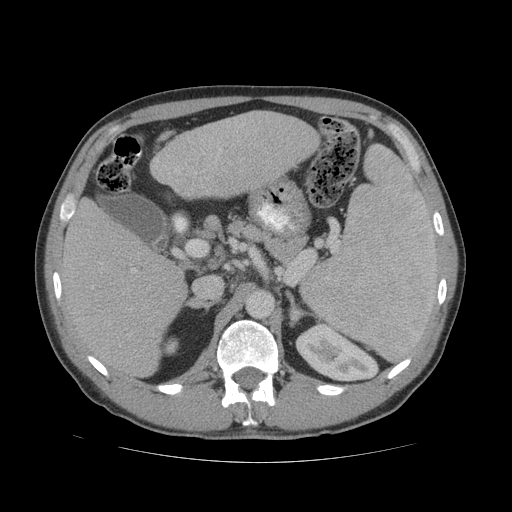
Contrast-enhanced abdominal CT (liver protocol), one axial slice. Slice 33 of 81 in the series (ordered by position). Reconstruction kernel STANDARD. Soft-tissue window (W 400 / L 40 HU). 2.5 mm slice thickness. 512 × 512 image matrix, field of view 400 × 400 mm. Case-level facts recorded for this patient, not image findings: diagnosis: hepatocellular carcinoma (patient treated with transarterial chemoembolisation; whether this scan precedes or follows treatment is not stated here); TNM stage (as recorded): Stage-IVB.
Structures marked on this image (semi-automatic segmentation, software-assisted and operator-edited):
- liver parenchyma outside the tumour (the mass and vessels are separate outlines, so this box may not span the whole liver): bounding box <58,110,320,376> (left, top, right, bottom; pixels)
- liver vessels: <133,123,245,272>